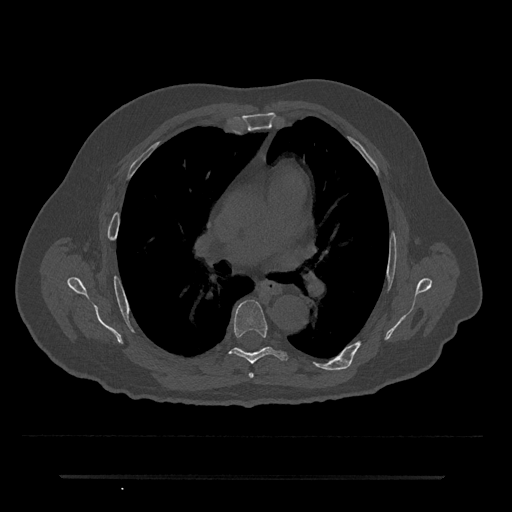
CT including the spine, one axial slice; position 434 of 797 along the scan axis; reconstruction kernel Br40s/3; bone window (W 1800 / L 400 HU); 0.5 mm slice thickness; 512 × 512 image matrix, field of view 437 × 437 mm. Male patient, age 69 years. From the clinical record (not read from this slice): primary cancer: prostate.
Structures marked on this image (semi-automatic segmentation, software-assisted and operator-edited):
- T5 vertebra: bounding box (x1, y1, x2, y2) in pixels: (248, 372, 254, 378)
- T6 vertebra: (230, 300, 287, 364)